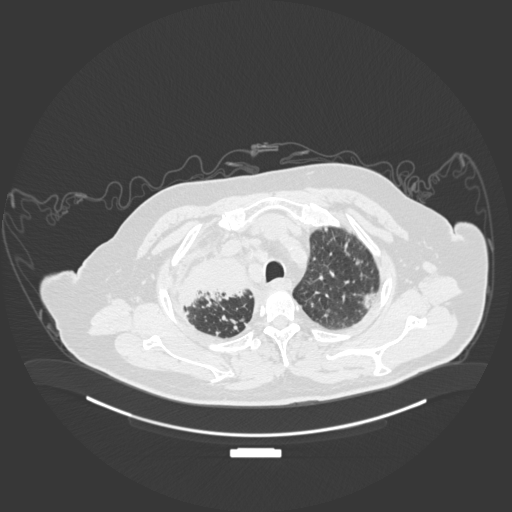
Chest CT, one axial slice; lung window (W 1500 / L -600 HU); 1 mm slice thickness; 512 × 512 image matrix, field of view 500 × 500 mm. Male patient, age 69 years. Case-level facts recorded for this patient, not image findings: clinical TNM (as recorded): T4 N3 M1.
Structures marked on this image (bounding box drawn by a radiologist):
- lung tumour (recorded histology: adenocarcinoma): bounding box [x1, y1, x2, y2] px = [173, 252, 257, 308]